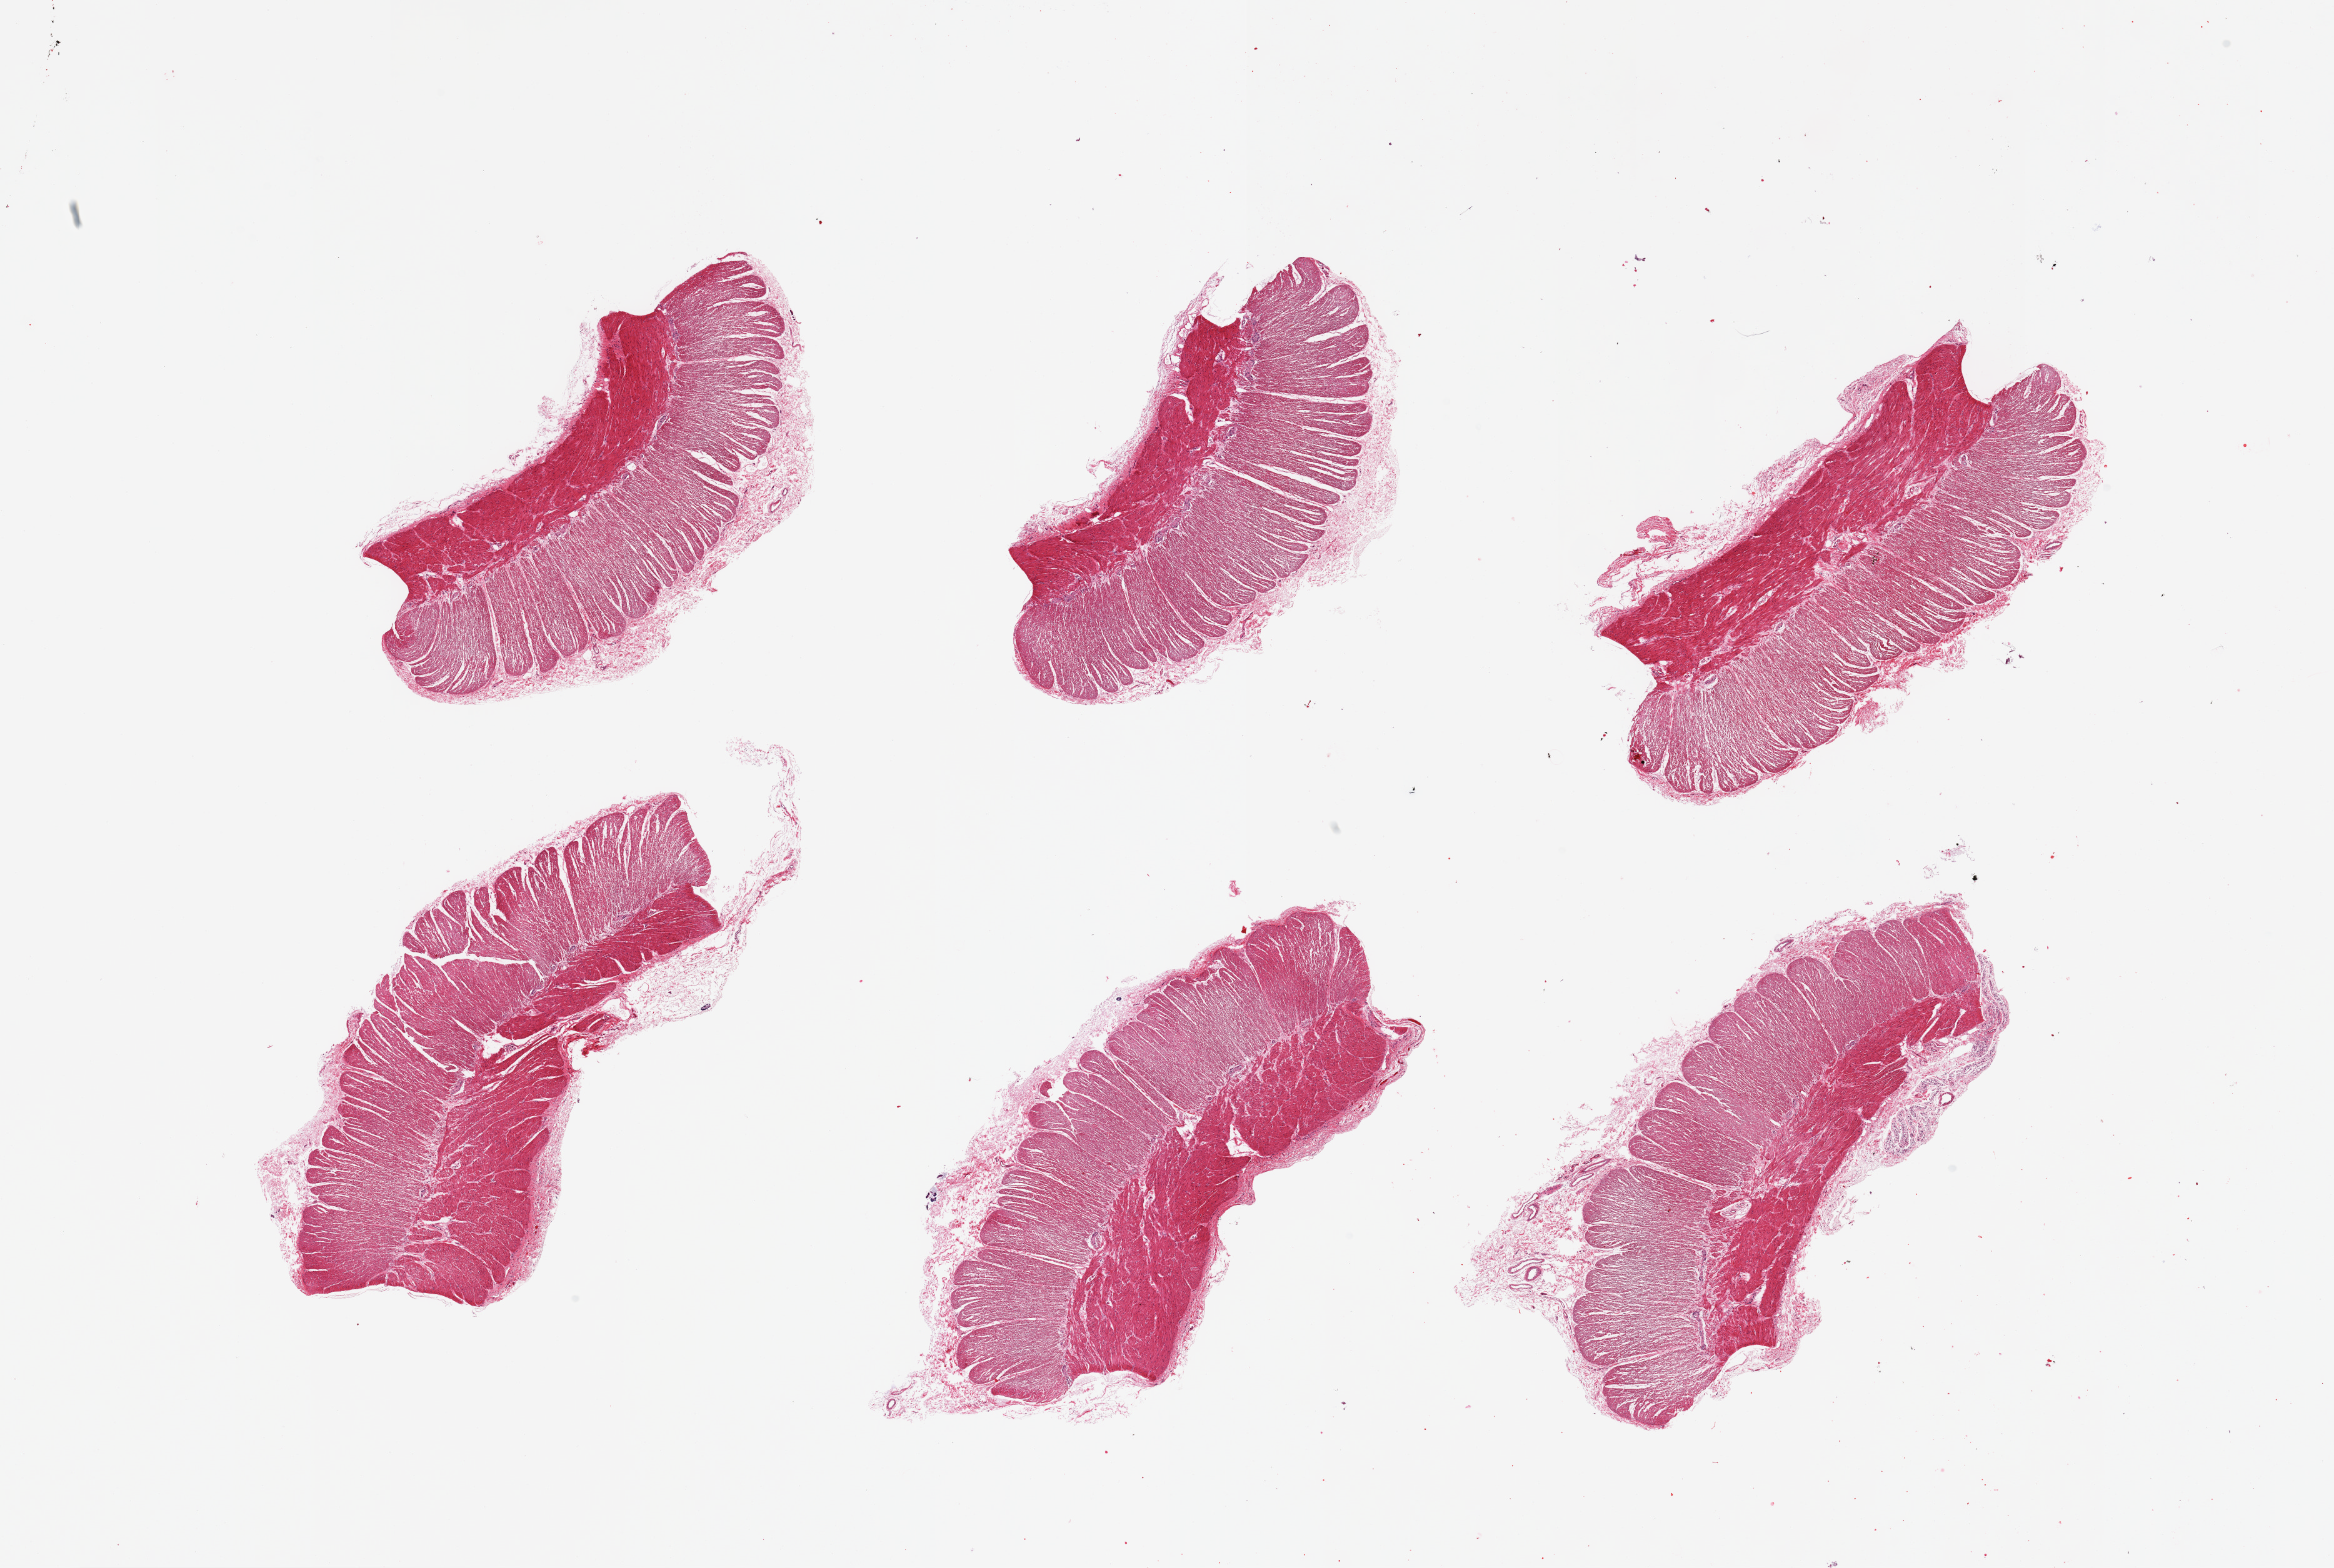
Hematoxylin and eosin (H&E) whole-slide image, a low-resolution overview of the entire scanned area, about 29.5 x 19.8 mm, PAXgene-fixed, paraffin-embedded tissue, sampled site (target tissue): sigmoid colon, donor tissue sample. Male donor.
Review note (as recorded): 6 pieces; target muscularis.